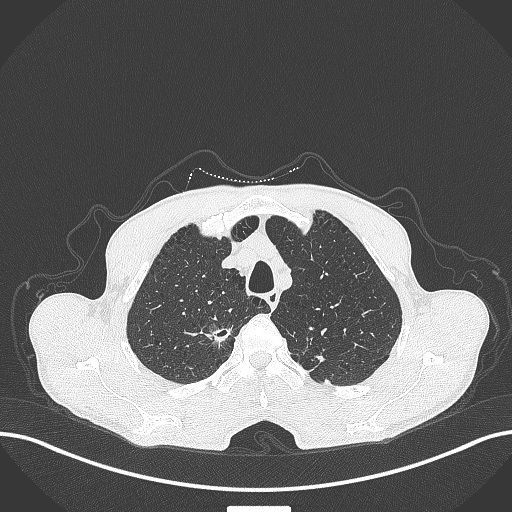
Chest CT, one axial slice. Slice 355 of 445 in the series (ordered by position). Reconstruction kernel B70f. 120 kVp. Lung window (W 1500 / L -600 HU). 512 × 512 image matrix, field of view 400 × 400 mm. Patient: male, 70 years. Case-level facts recorded for this patient, not image findings: clinical TNM (as recorded): T1a N0 M0; histopathological grade: G1-2.
Structures marked on this image (bounding box drawn by a radiologist):
- lung tumour (recorded histology: adenocarcinoma): box from (x=201, y=318) to (x=233, y=351) px